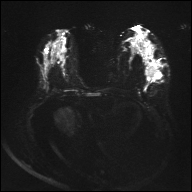
Breast MRI, one axial slice; slice 16 of 32 in the series (ordered by position); diffusion-weighted series; image 2 of 4 stored at this slice position (different b-values; order by instance number); 1.5 T; 4 mm slice thickness; 192 × 192 image matrix, field of view 360 × 360 mm. Female patient.
Structures marked on this image (manually delineated by an expert):
- tumour on diffusion-weighted imaging: bounding box <147,67,160,77> (left, top, right, bottom; pixels)